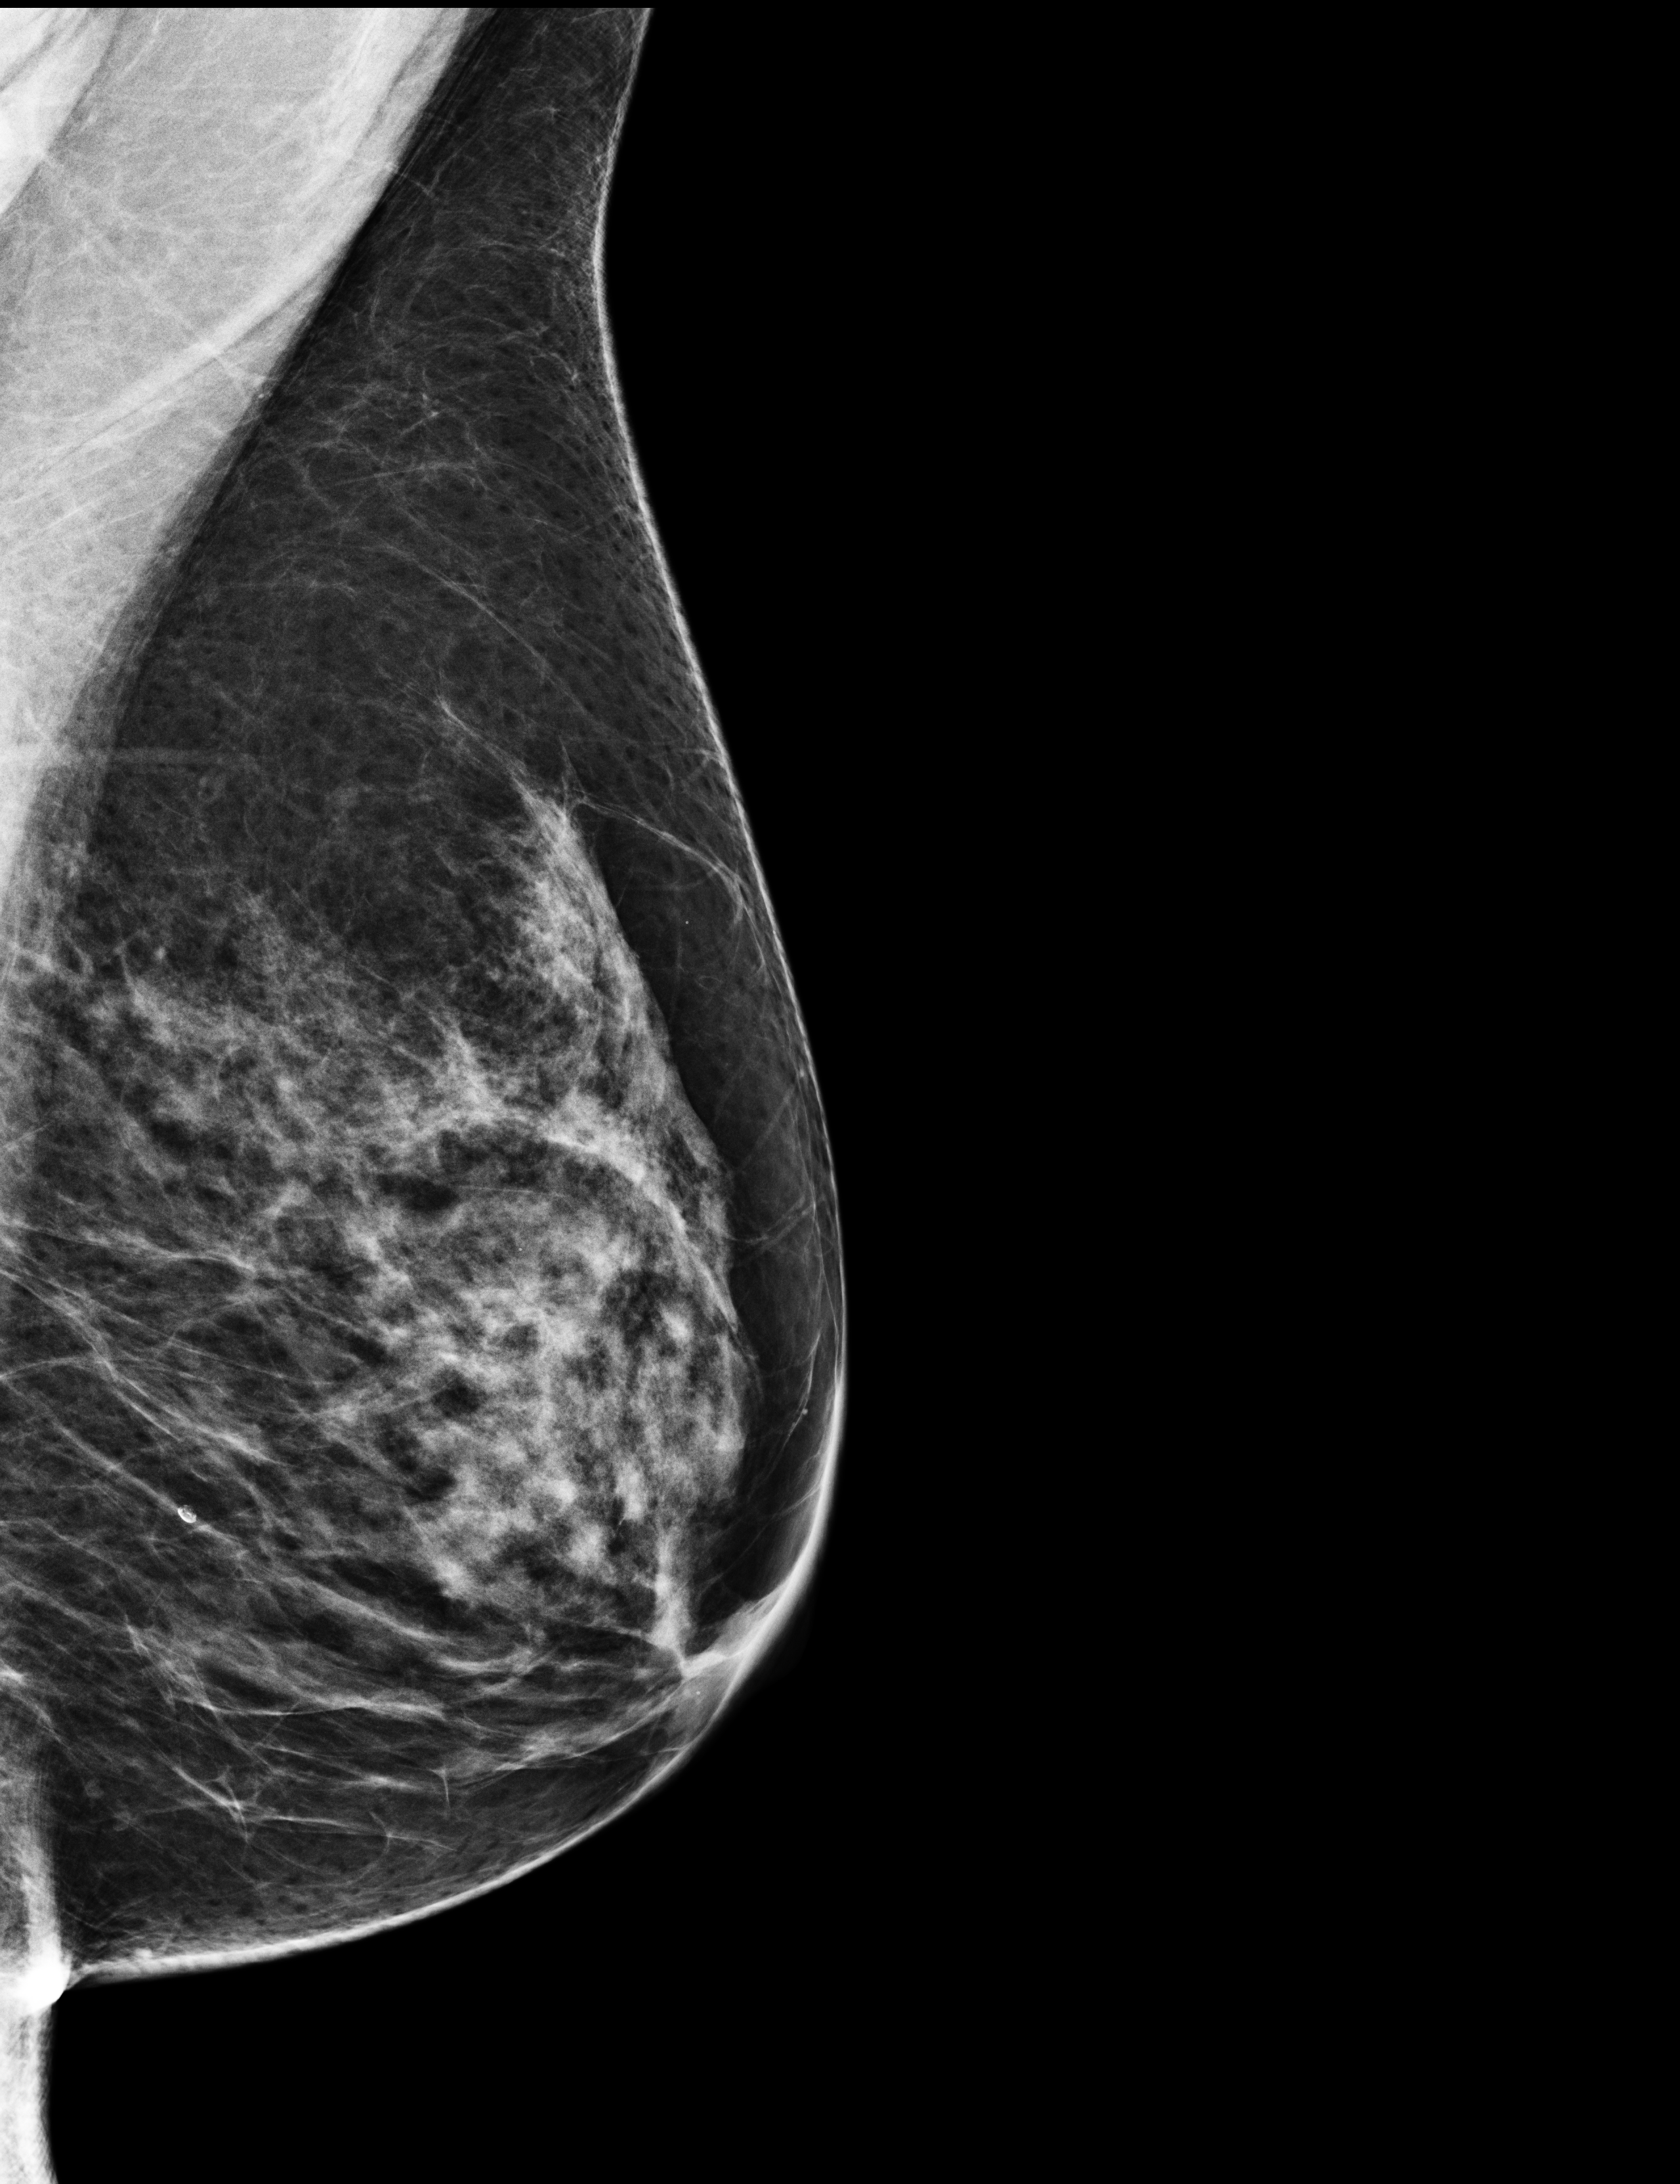
Full-field digital mammogram (FFDM); left breast; MLO view; screening examination; system: Selenia Dimensions. Female patient, age 66 years.
- breast density at the screening exam (both breasts): heterogeneously dense (BI-RADS density category c)
- final BI-RADS assessment for this screening round (tomosynthesis exam, both breasts): category 1
- recall: no recall after this screen